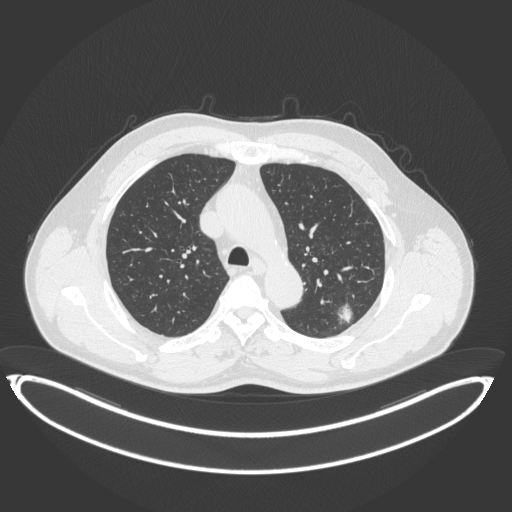
Chest CT, one axial slice. Slice 258 of 399 in the series (ordered by position). Reconstruction kernel B31f. 120 kVp. Lung window (W 1500 / L -600 HU). 512 × 512 image matrix. Male patient, age 58 years. Case-level facts recorded for this patient, not image findings: clinical TNM (as recorded): T1c N0 M0.
Outlined on this slice (bounding box drawn by a radiologist):
- lung tumour (recorded histology: adenocarcinoma): bounding box <333,299,362,330> (left, top, right, bottom; pixels)